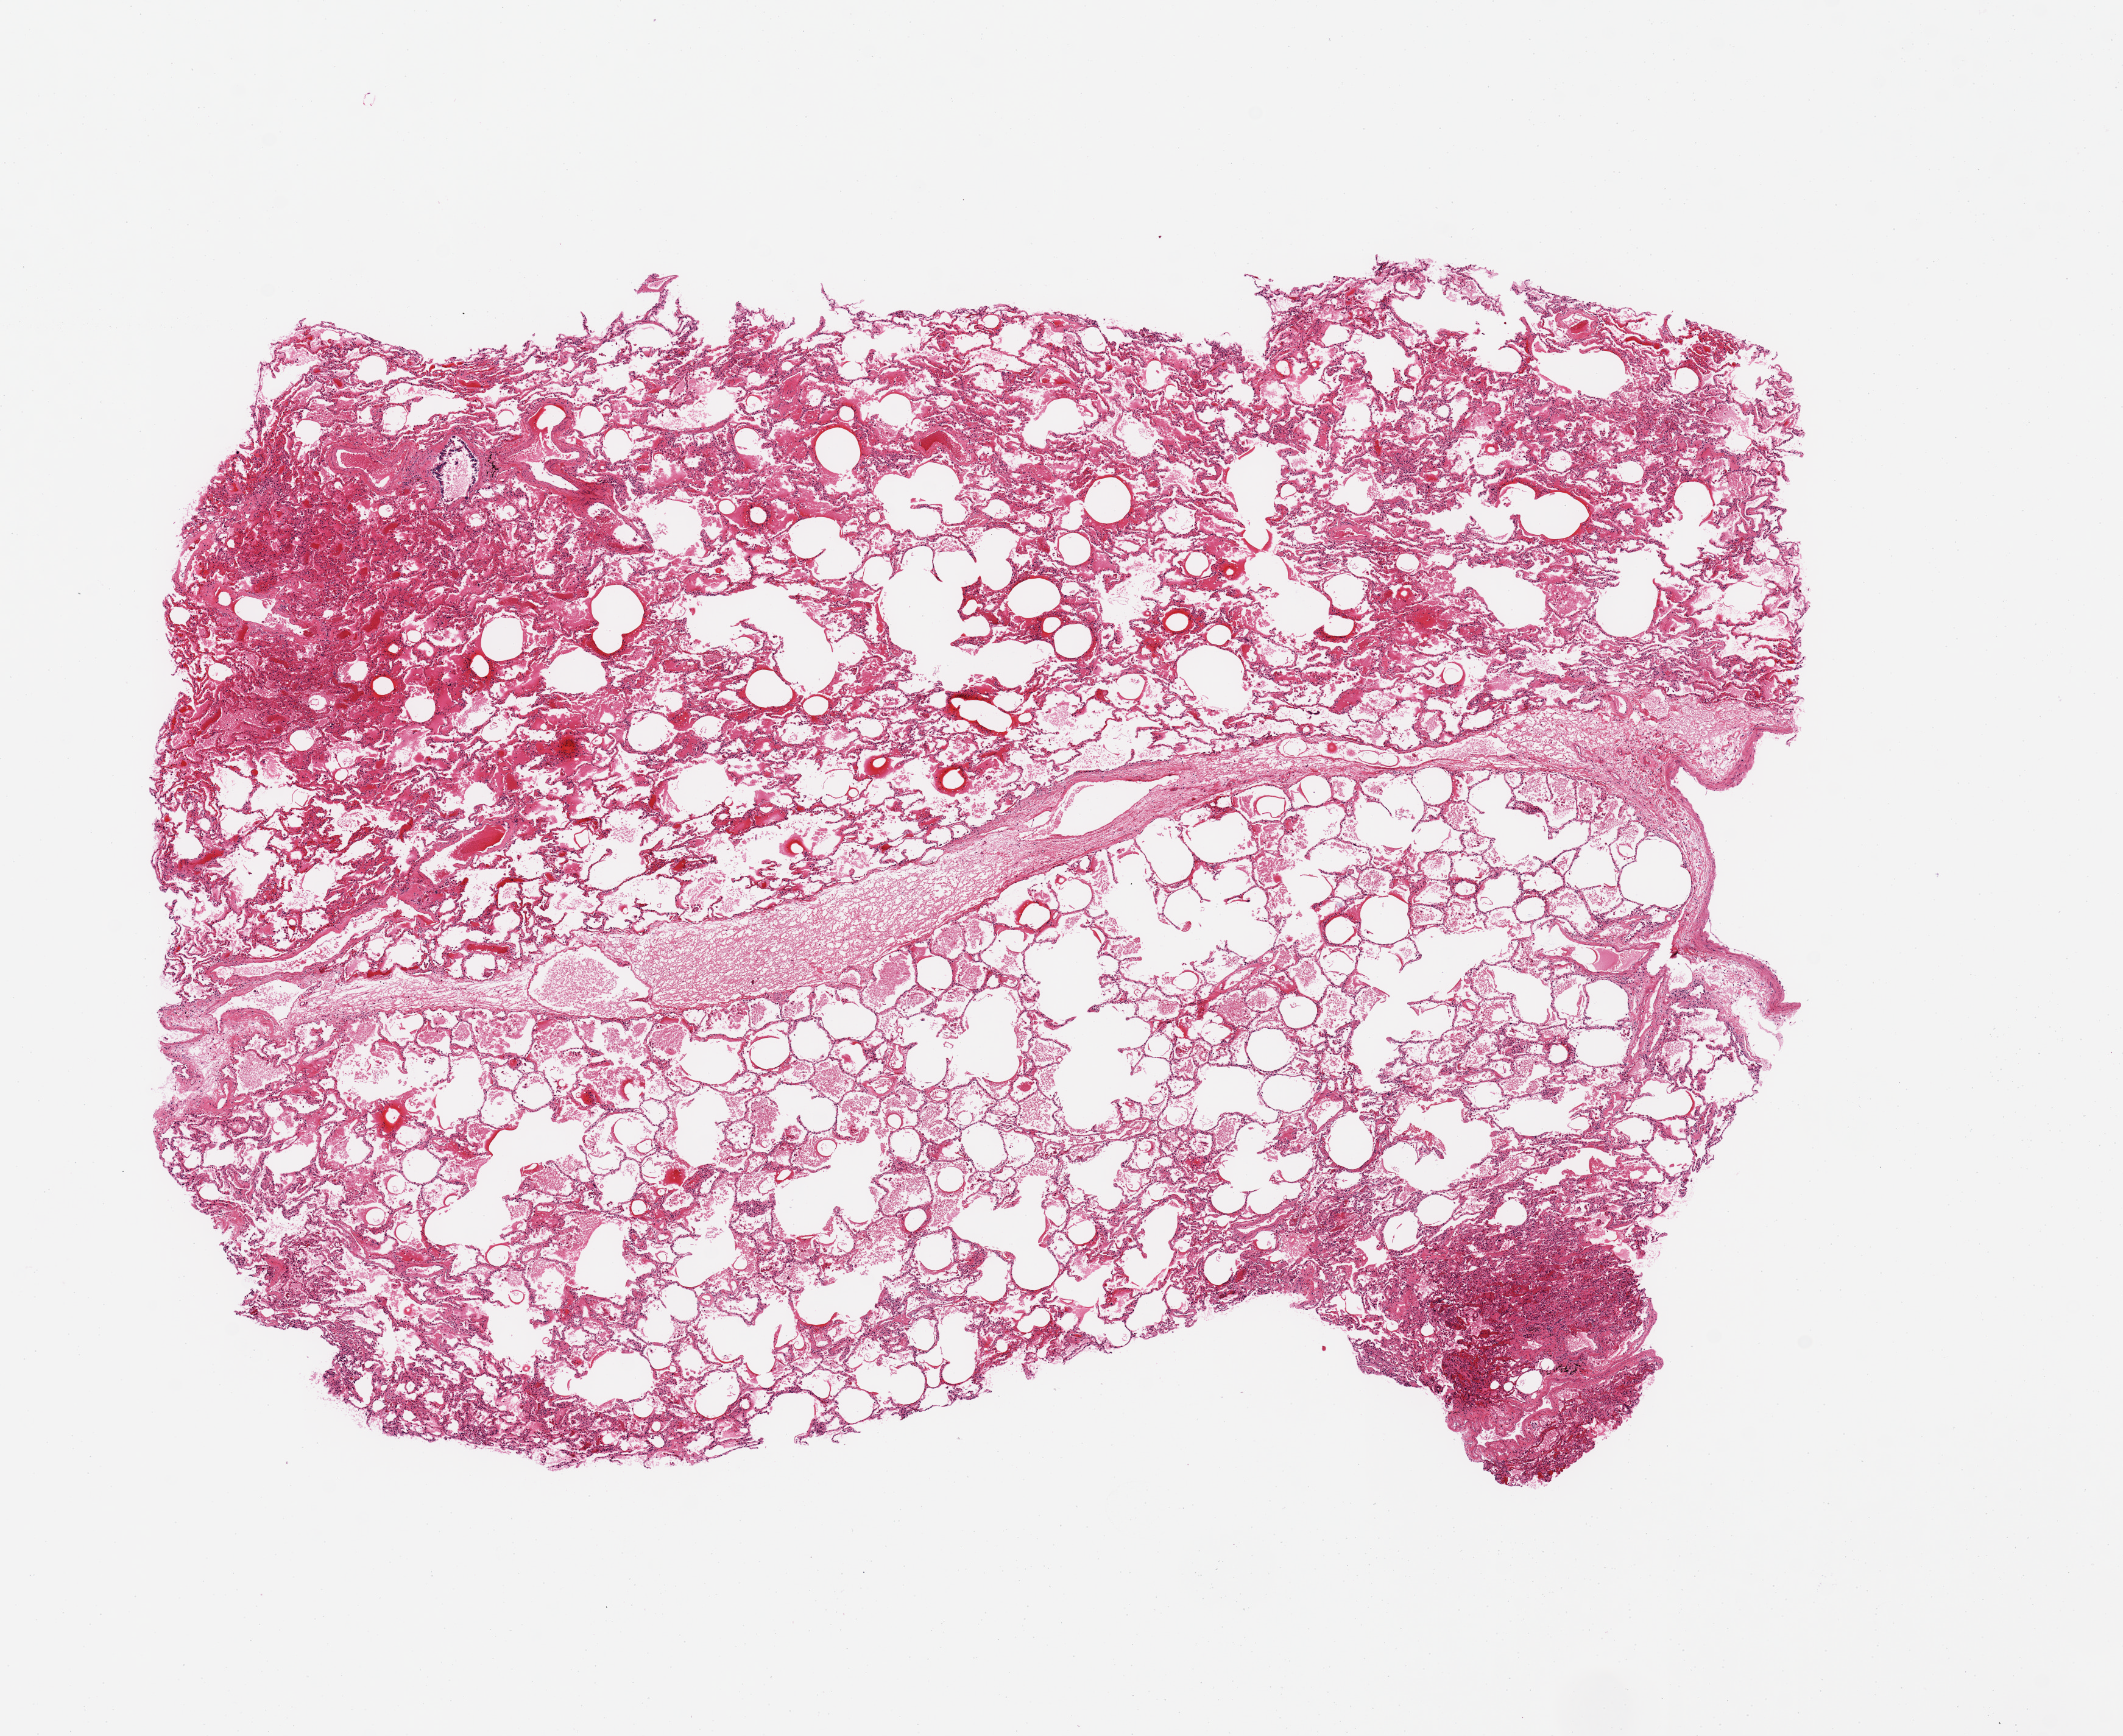
Digitized hematoxylin and eosin (H&E)-stained section, brightfield — low-resolution overview of the scanned area, about 13.8 x 11.3 mm (slide scanned at 20x), PAXgene-fixed, paraffin-embedded tissue, section of lung (target tissue), donor tissue sample. Donor: male.
Reviewer comment on this tissue sample: Mild congestion/edema.